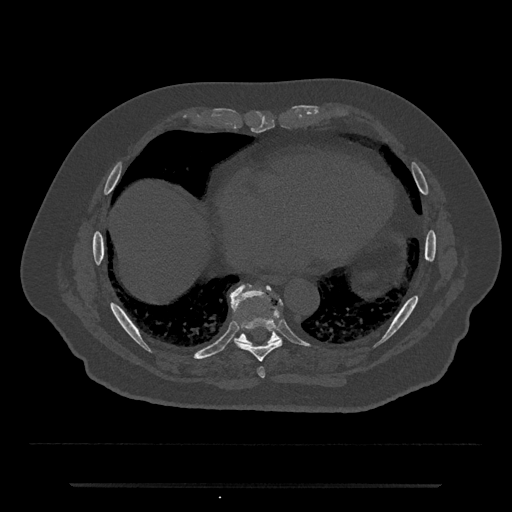
CT including the spine, one axial slice. Position 791 of 797 along the scan axis. Reconstruction kernel Br40s/3. 120 kVp. Bone window (W 1800 / L 400 HU). 0.5 mm slice thickness. 512 × 512 image matrix, field of view 434 × 434 mm. Patient: male, 80 years. Case-level facts recorded for this patient, not image findings: primary cancer: prostate.
Structures marked on this image (semi-automatically segmented with operator editing):
- T8 vertebra: box from (x=235, y=315) to (x=282, y=362) px
- T9 vertebra: (x=230, y=284)–(x=281, y=347)